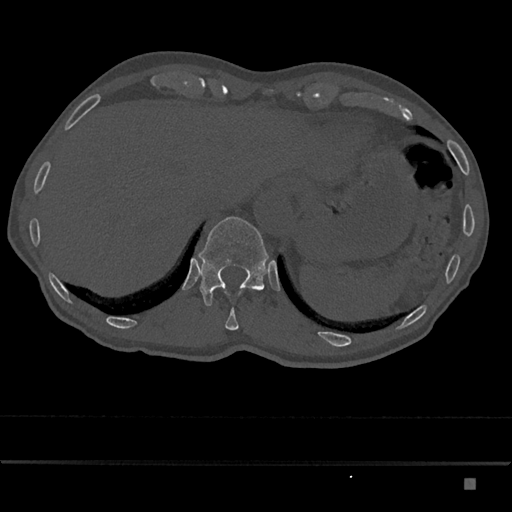
CT including the spine, one axial slice. Slice 636 of 797 in the series (ordered by position). Bone window (W 1800 / L 400 HU). 512 × 512 image matrix, field of view 390 × 390 mm. Patient: male, 72 years. Case-level facts recorded for this patient, not image findings: primary cancer: prostate.
Annotated regions visible in this slice (semi-automatic segmentation, software-assisted and operator-edited):
- T11 vertebra: bounding box [x1, y1, x2, y2] px = [225, 308, 239, 330]
- T12 vertebra: [199, 216, 269, 306]